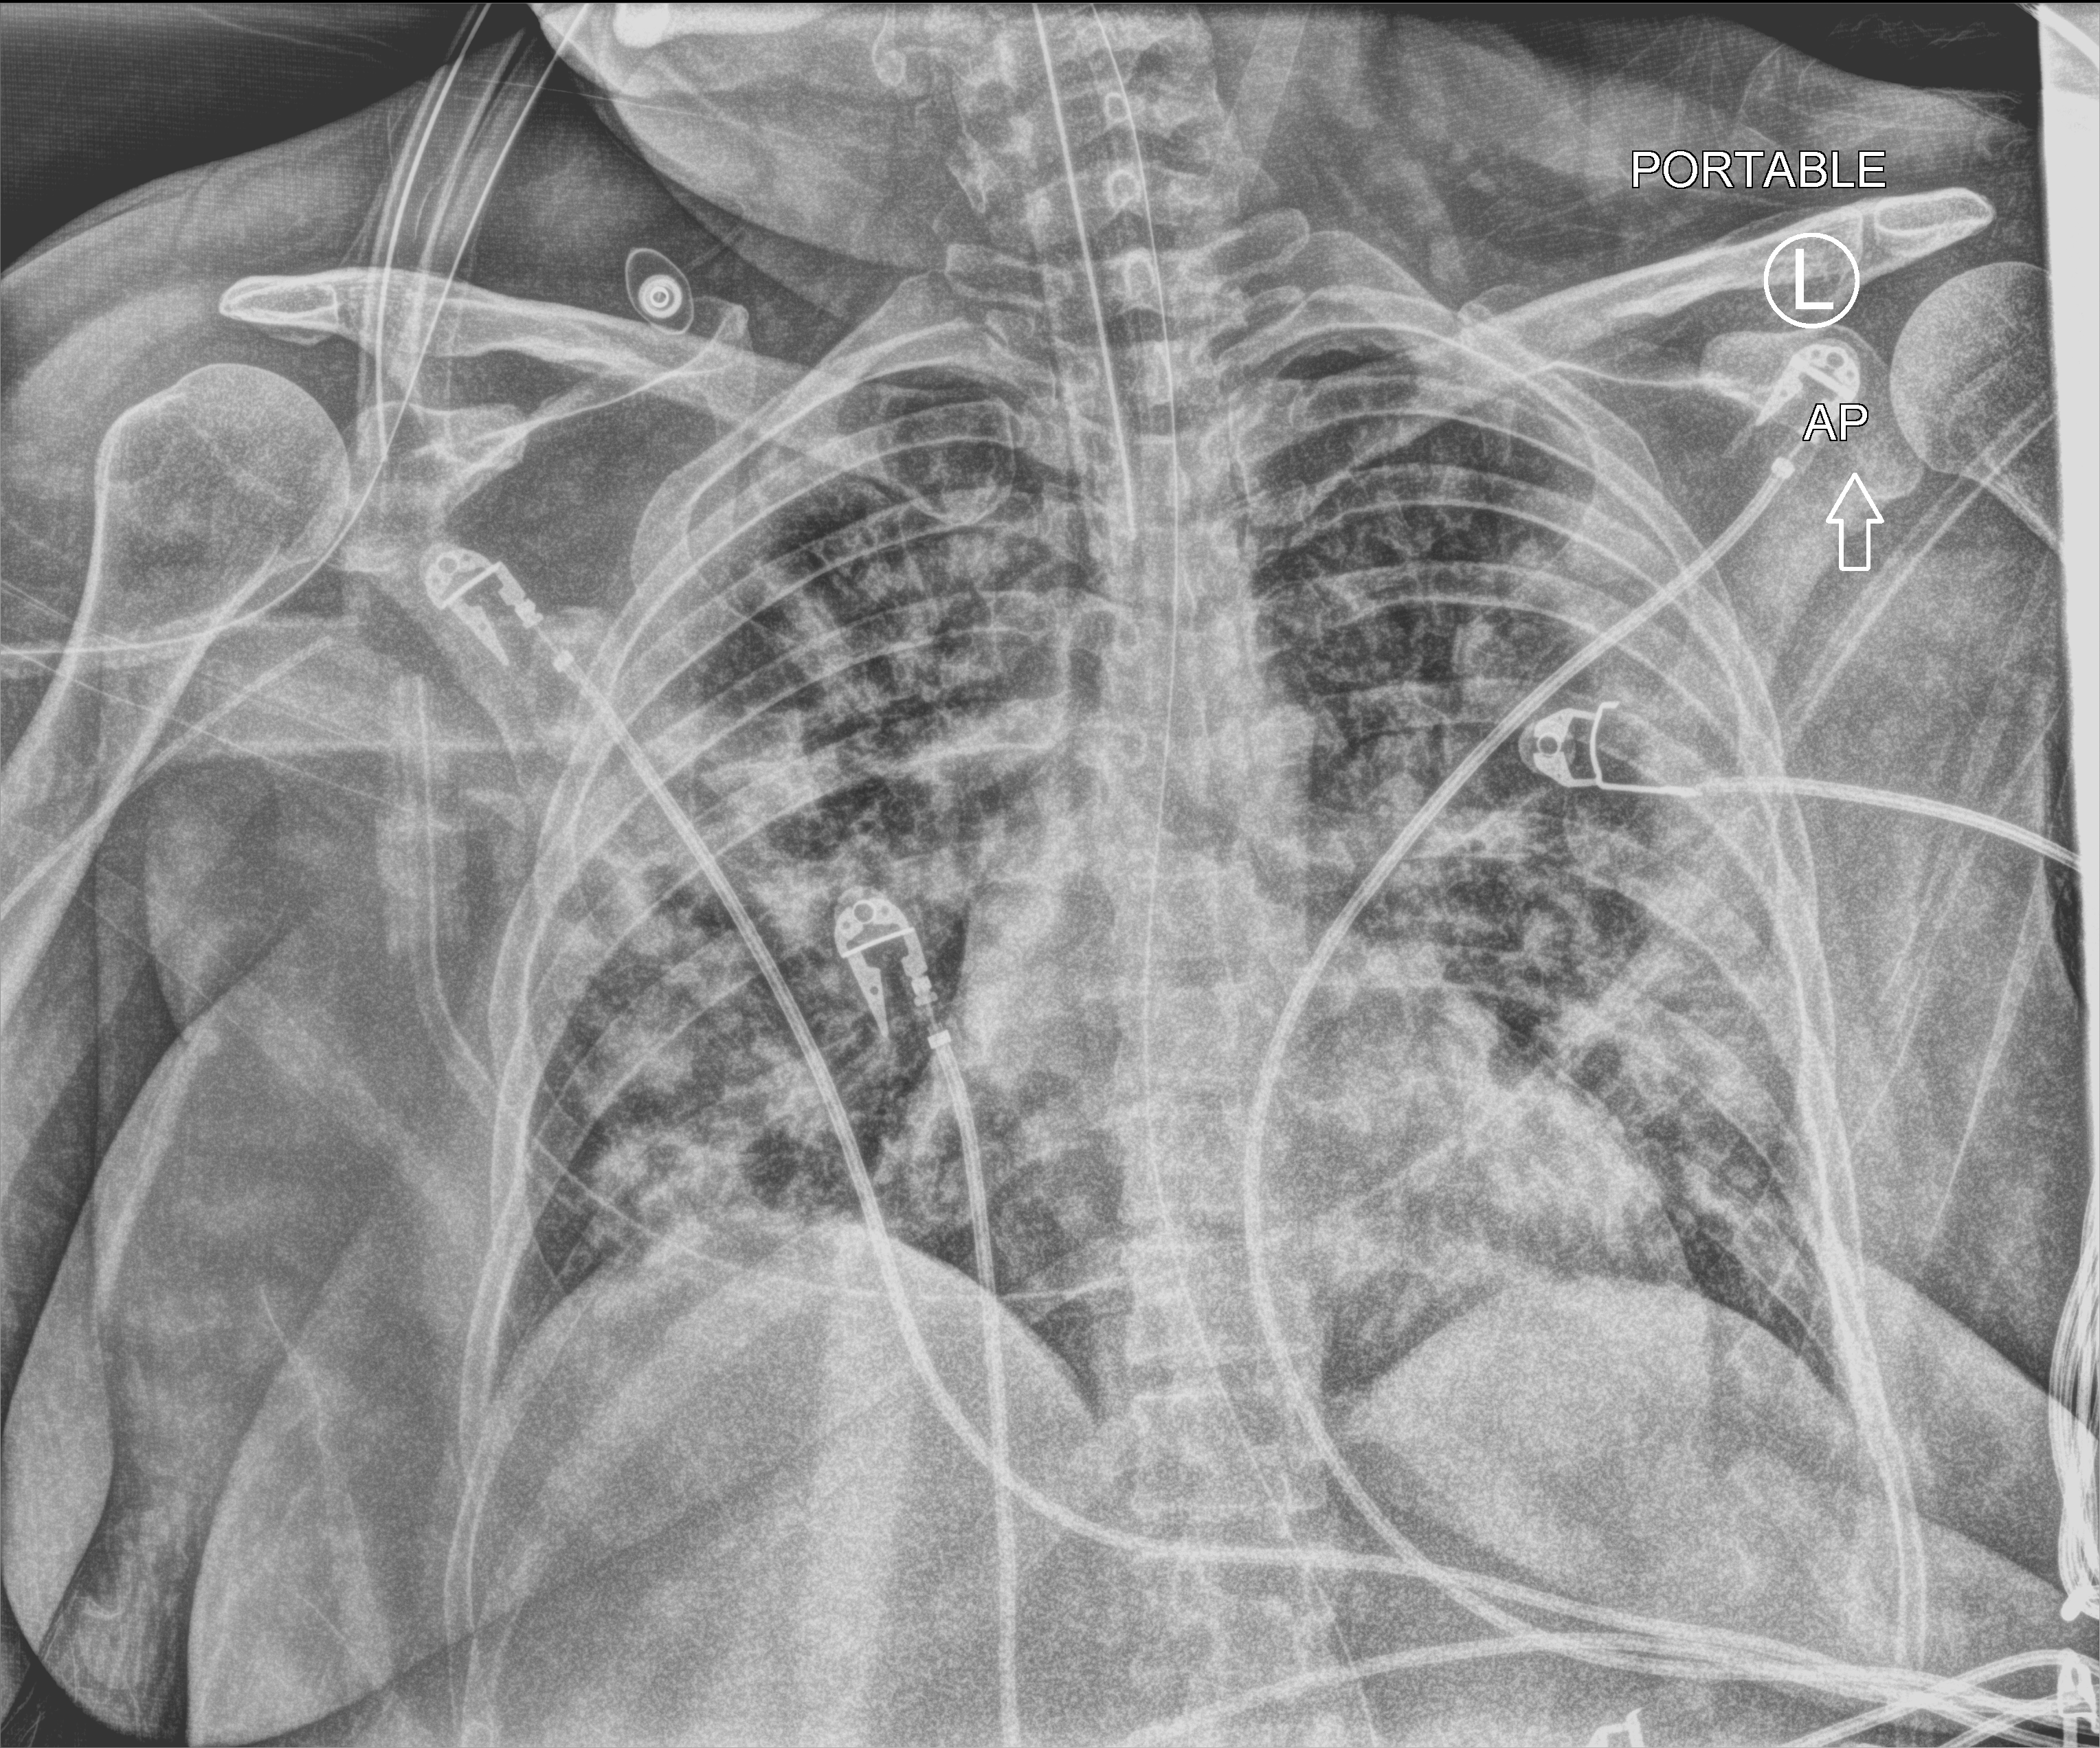
Bedside chest radiograph (computed radiography); anteroposterior (AP) projection. Female patient hospitalised with COVID-19, age 18–59 years.
From the hospital-stay record, not from the radiograph (when in the stay this image was taken is not recorded): chronic kidney disease (admission record): no; COPD (admission record): no; mechanically ventilated during this hospital stay: yes.